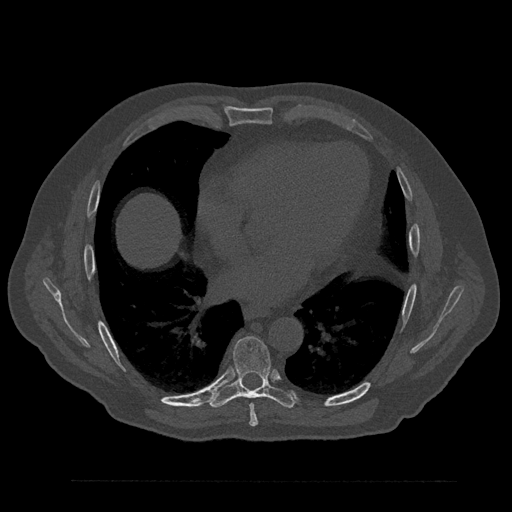
CT including the spine, one axial slice; position 466 of 797 along the scan axis; reconstruction kernel Br40s/3; 120 kVp; bone window (W 1800 / L 400 HU); 512 × 512 image matrix, field of view 430 × 430 mm. Male patient, age 61 years. Case-level facts recorded for this patient, not image findings: primary cancer: prostate.
Outlined on this slice (semi-automatically segmented with operator editing):
- T7 vertebra: bounding box (x1, y1, x2, y2) in pixels: (249, 403, 258, 427)
- T8 vertebra: (210, 336, 296, 408)